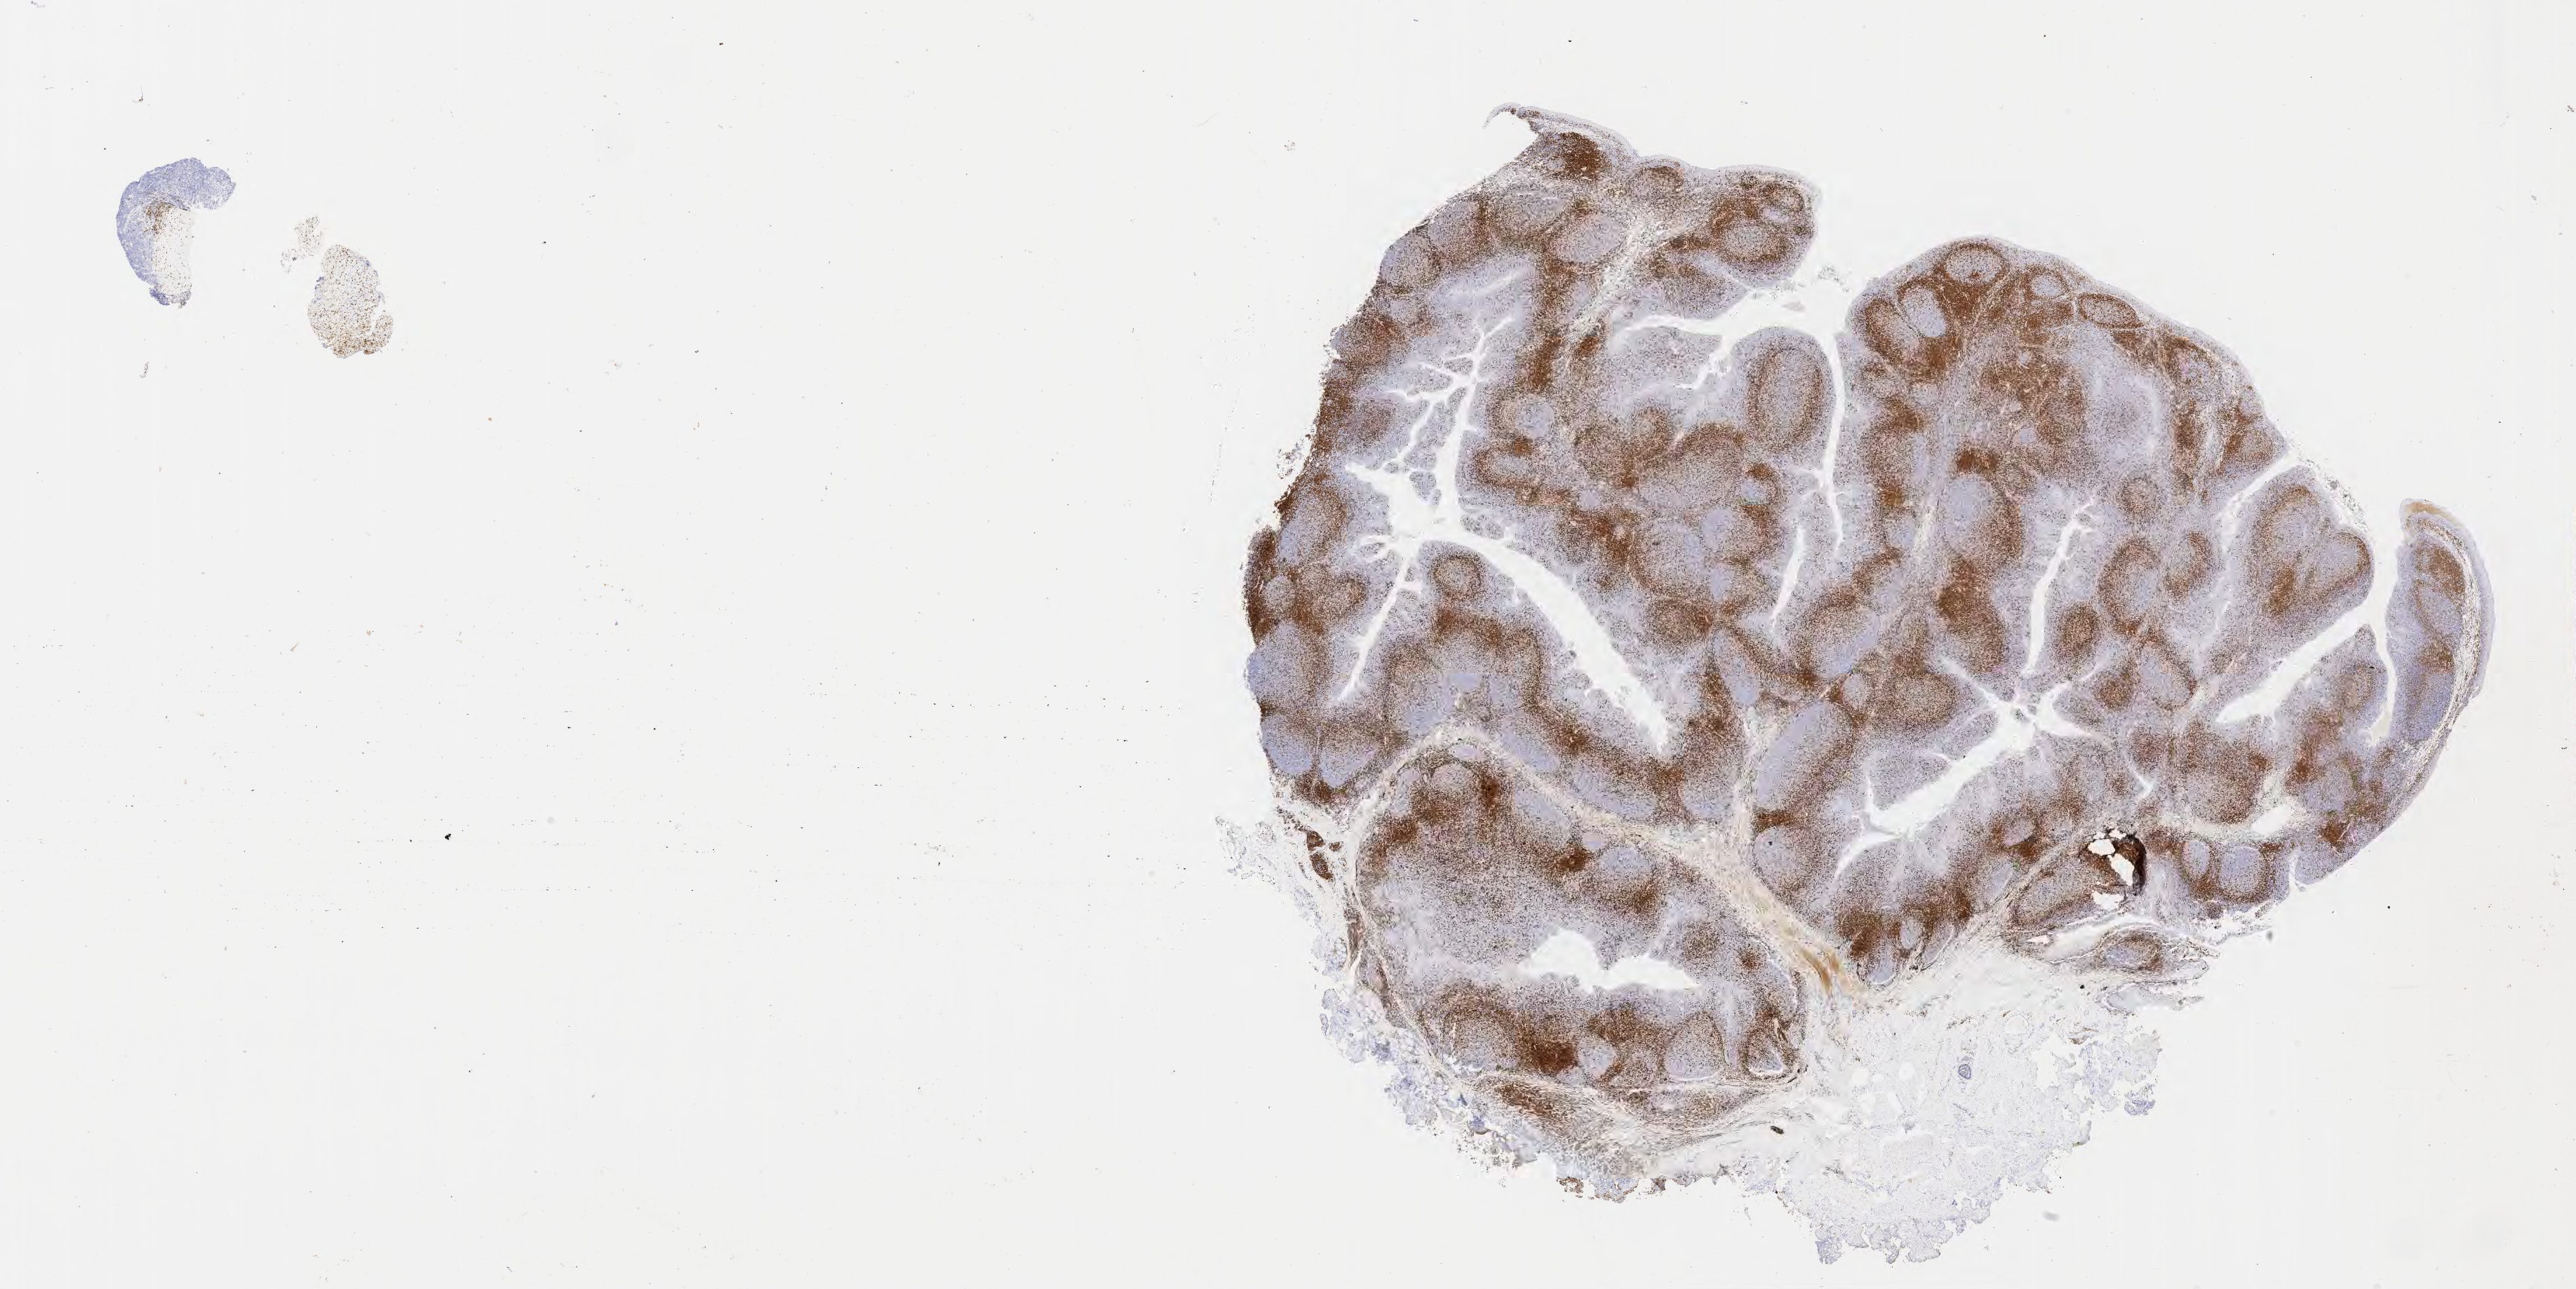
IHC for CD3, whole-slide image — low-resolution overview of the scanned area, about 29.7 x 14.9 mm. Tumor tissue. Anatomic site: abdomen proper. Female, age 6 years at initial diagnosis.
* diagnosis: Diffuse large B-cell lymphoma, NOS